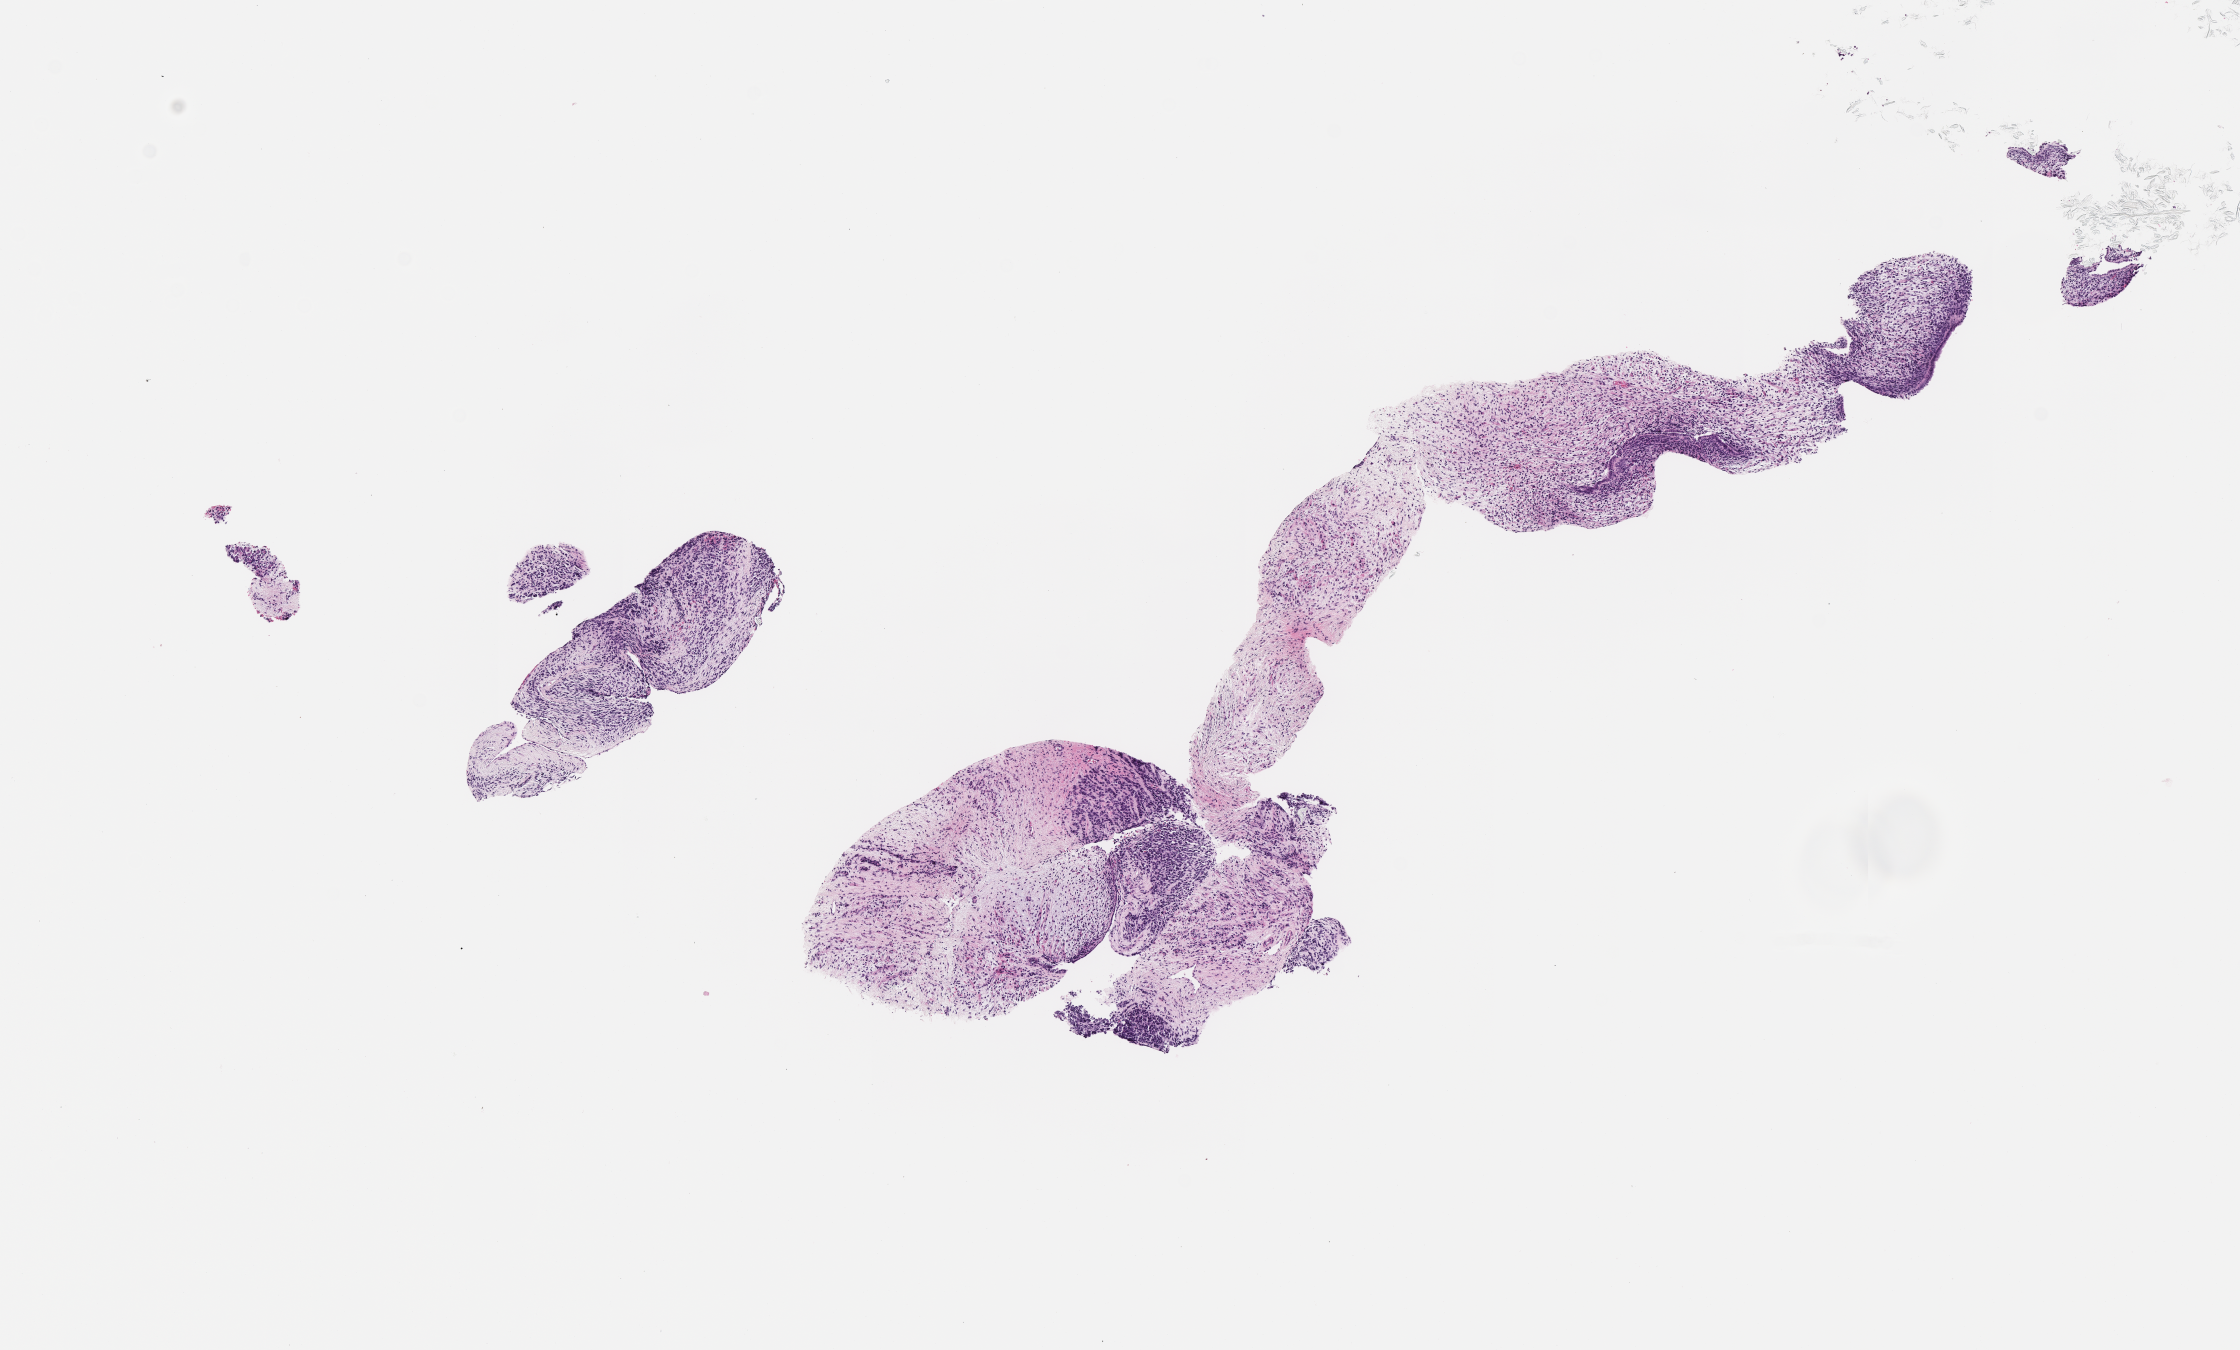
Digitized haematoxylin and eosin-stained section of tumor tissue, shown as a low-resolution overview of the whole scanned area (about 9.1 x 5.5 mm), formalin-fixed, paraffin-embedded (FFPE) tissue. Patient: male, age 6.9 years at diagnosis.
Diagnosis: rhabdomyosarcoma; histological classification: botryoid.